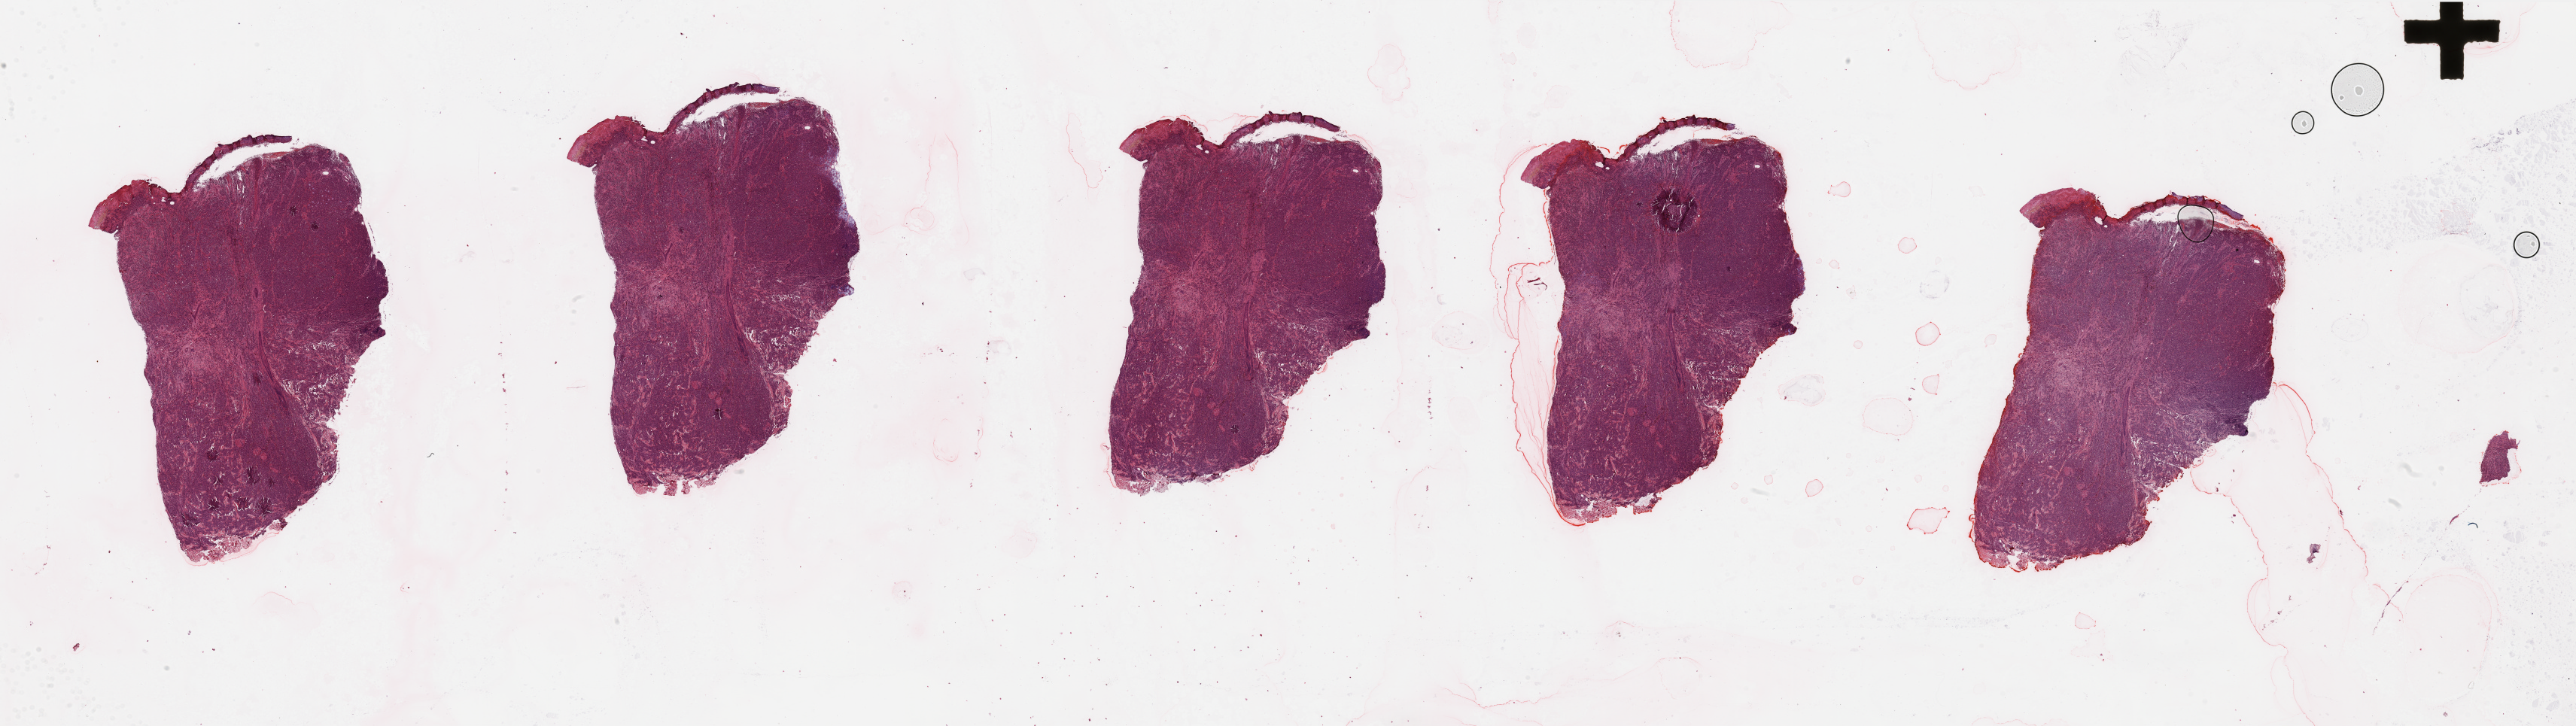
H&E-stained whole-slide image — low-resolution overview of the scanned area, about 54.1 x 15.3 mm; melanoma tumour tissue; sampled site not recorded. Patient: male, age 42 years.
- primary tumour site (as recorded): trunk
- AJCC pathologic stage: IIC
- histologic diagnosis: Malignant melanoma, NOS